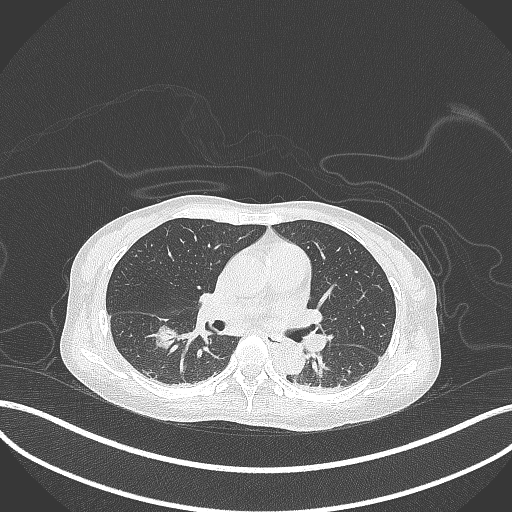
Chest CT, one axial slice; position 168 of 261 along the scan axis; reconstruction kernel B70f; lung window (W 1500 / L -600 HU); 1 mm slice thickness; 512 × 512 image matrix. Patient: female, 44 years. Case-level facts recorded for this patient, not image findings: clinical TNM (as recorded): T1c N0 M0.
Outlined on this slice (bounding box drawn by a radiologist):
- lung tumour (recorded histology: adenocarcinoma): bounding box [x1, y1, x2, y2] px = [151, 320, 176, 350]